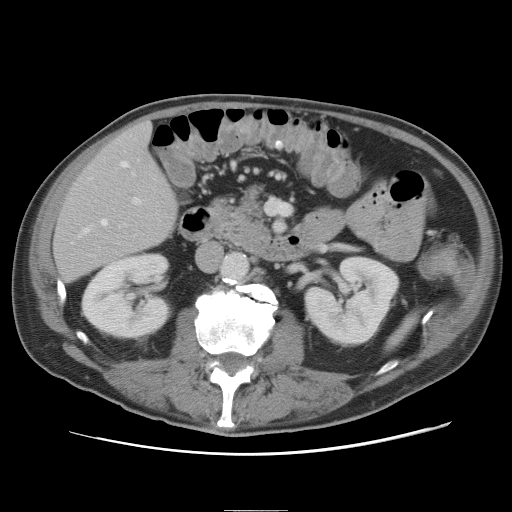
Contrast-enhanced abdominal CT, one axial slice. Slice 24 of 89 in the series (ordered by position). Intravenous contrast given. Soft-tissue window (W 400 / L 40 HU). 5 mm slice thickness. 512 × 512 image matrix, field of view 375 × 375 mm. Male patient, age 69 years. Case-level facts recorded for this patient, not image findings: diagnosis: colorectal cancer liver metastases, imaged before liver resection; multiple liver metastases: no; largest metastasis: 8.5 cm; disease in both lobes: no.
Structures marked on this image (expert manual segmentation):
- hepatic veins: box from (x=83, y=161) to (x=129, y=233) px
- liver: (x=54, y=122)–(x=177, y=281)
- planned liver remnant (the part of the liver to remain after resection): (x=55, y=122)–(x=177, y=281)
- portal vein (with intrahepatic branches): (x=132, y=197)–(x=142, y=205)